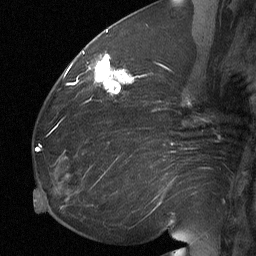
Breast MRI (dynamic contrast-enhanced), one sagittal slice; position 29 of 64 along the scan axis; dynamic contrast-enhanced study with each time point stored as its own series, time point 2 of 3 at this slice position (early post-contrast, ordered by acquisition time); 1.5 T; TE 4.8 ms, TR 27 ms; 2 mm slice thickness; 256 × 256 image matrix, field of view 200 × 200 mm. Patient: female, 60 years. From the clinical record (not read from this slice): setting: breast cancer imaged before/during neoadjuvant chemotherapy; receptor status: HR-positive, HER2-negative.
Annotated regions visible in this slice (semi-automatically segmented with operator editing):
- analysis volume of interest (the breast-tissue region the enhancement analysis was run in; not a lesion): bounding box (x1, y1, x2, y2) in pixels: (91, 56, 133, 101)
- tumour enhancement mask (voxels above the 90 % enhancement threshold inside the analysis volume of interest): (94, 56, 133, 94)